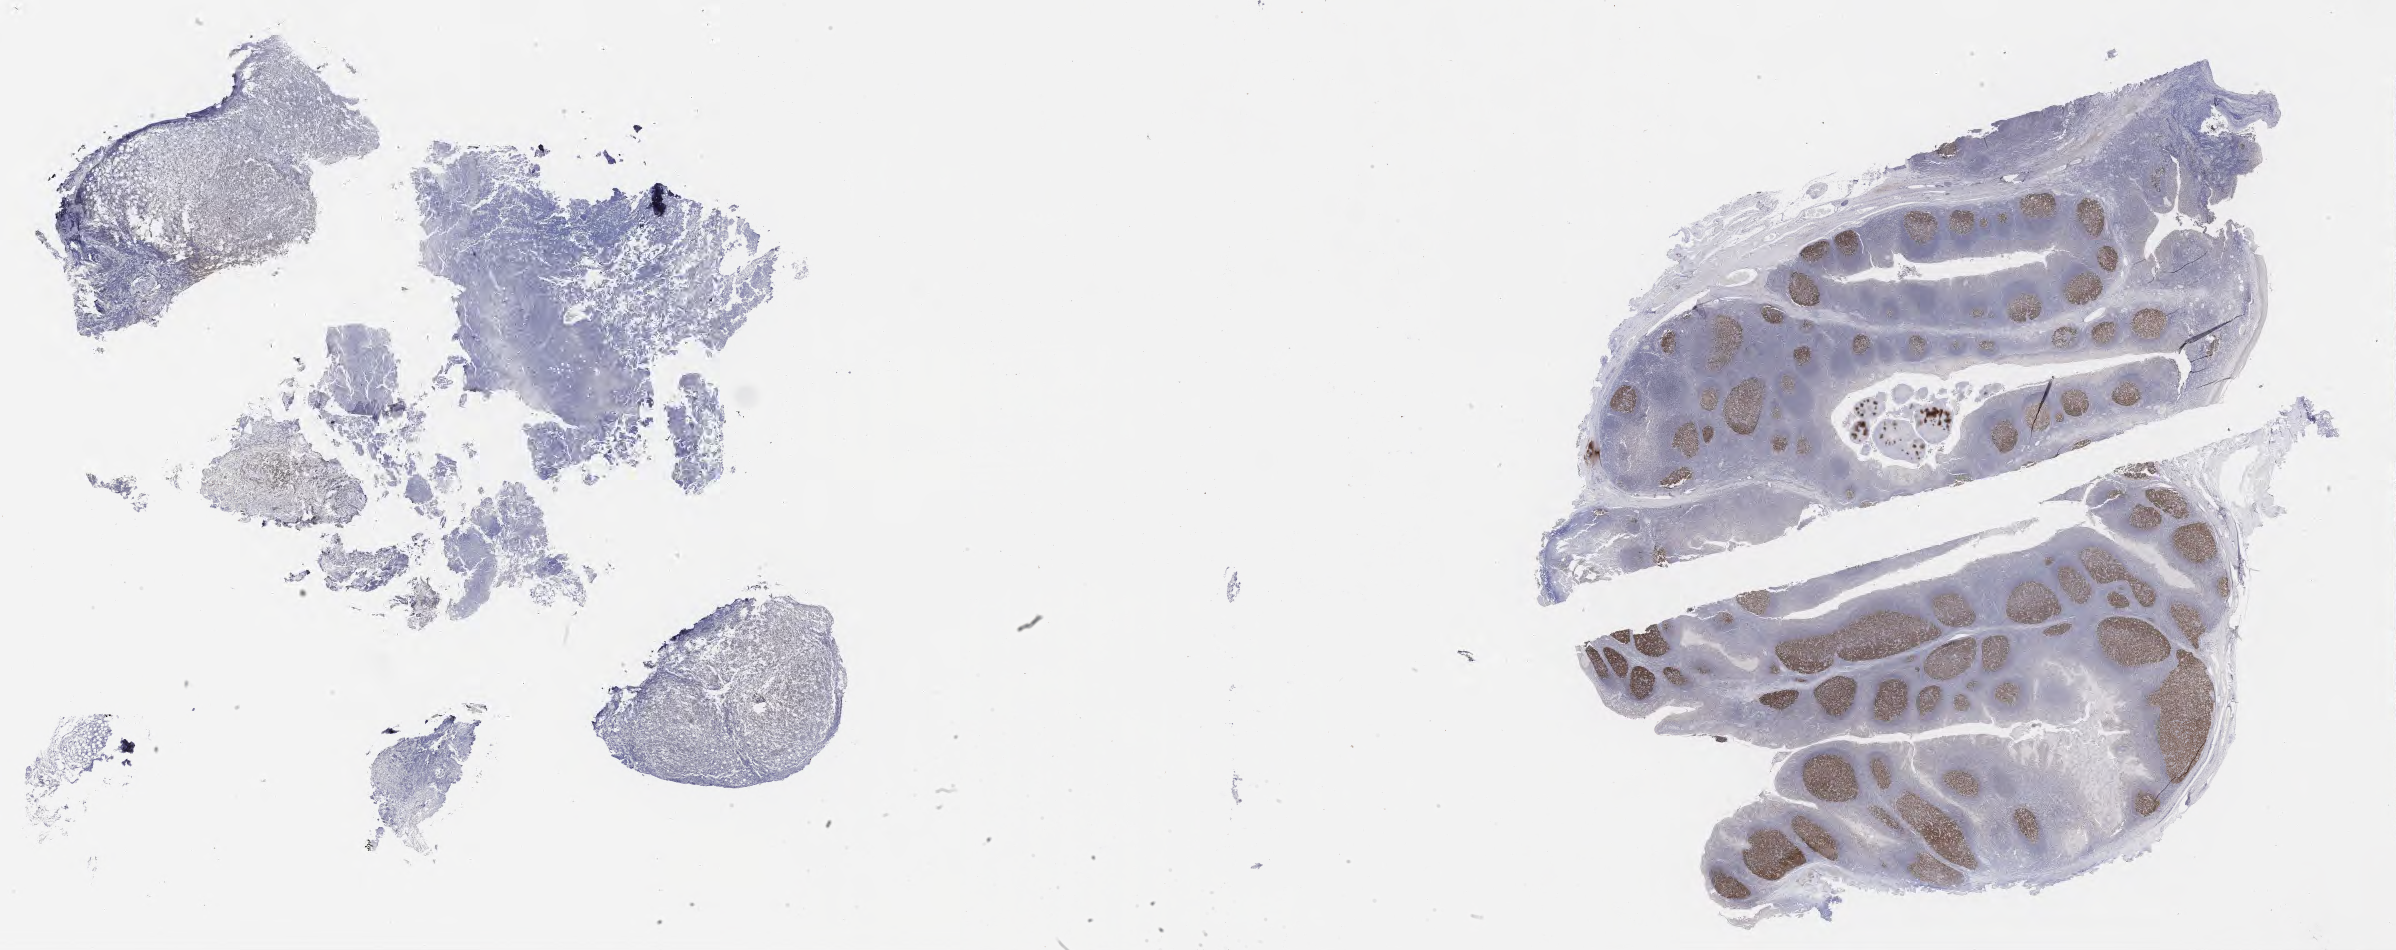
IHC for BCL6, whole-slide image — whole scanned area (about 38.7 x 15.4 mm) shown as a low-resolution overview, specimen: tumor tissue. Patient: male, age 23 years.
Diagnosis: Burkitt lymphoma, NOS.